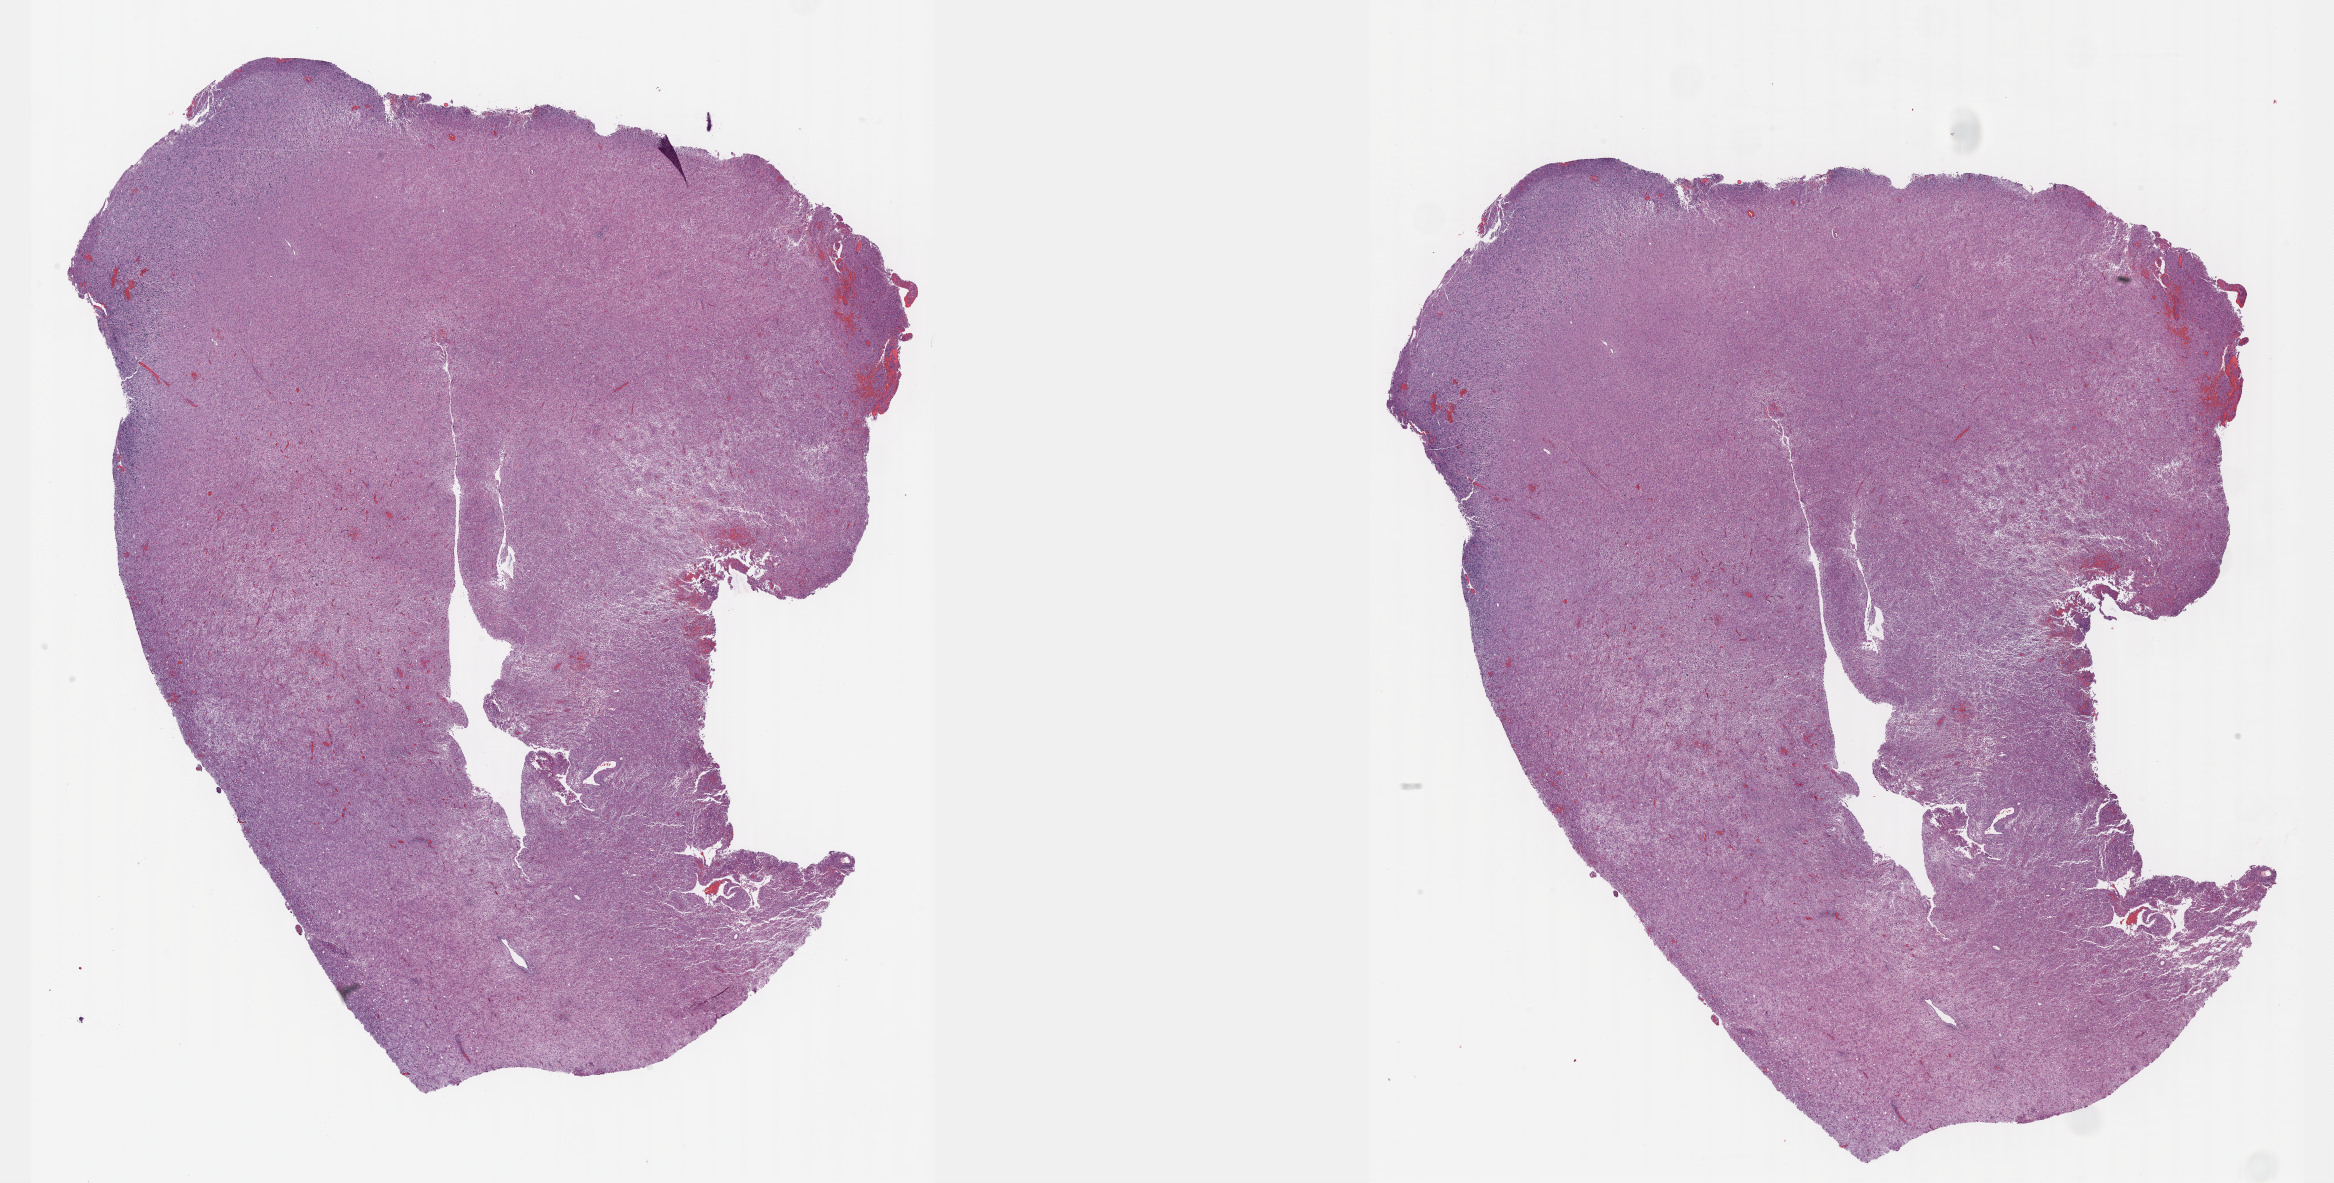
Digitized Hematoxylin and eosin (H&E) stained tissue section (whole slide), whole scanned area (about 37.7 x 19.1 mm, slide scanned at 40x) shown as a low-resolution overview. FFPE section. Primary tumour sample from the brain. Patient: female, age at initial diagnosis 52 years. Histologic grade: G3 (poorly differentiated).
* pathologic diagnosis: Astrocytoma, anaplastic (cerebrum)
* laterality: right